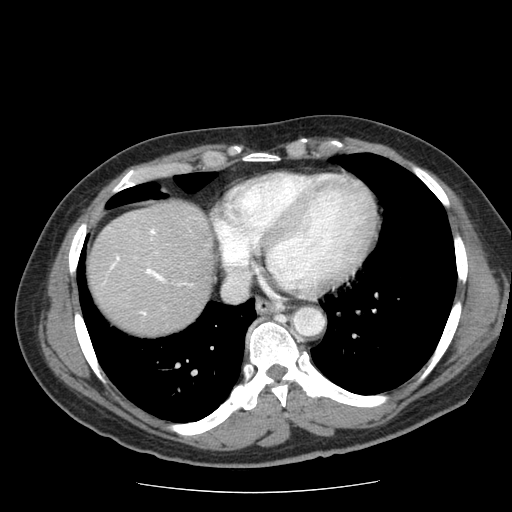
Contrast-enhanced abdominal CT (liver protocol), one axial slice. Position 67 of 85 along the scan axis. Reconstruction kernel STANDARD. 120 kVp. Soft-tissue window (W 400 / L 40 HU). 2.5 mm slice thickness. 512 × 512 image matrix, field of view 360 × 360 mm. From the clinical record (not read from this slice): diagnosis: hepatocellular carcinoma (patient treated with transarterial chemoembolisation; whether this scan precedes or follows treatment is not stated here); TNM stage (as recorded): Stage-IIIA; Child-Pugh class: A; tumour differentiation: well differentiated; tumour nodularity: multinodular.
Outlined on this slice (semi-automatic segmentation, software-assisted and operator-edited):
- liver parenchyma outside the tumour (the mass and vessels are separate outlines, so this box may not span the whole liver): bounding box <88,200,214,334> (left, top, right, bottom; pixels)
- liver vessels: <111,229,165,315>